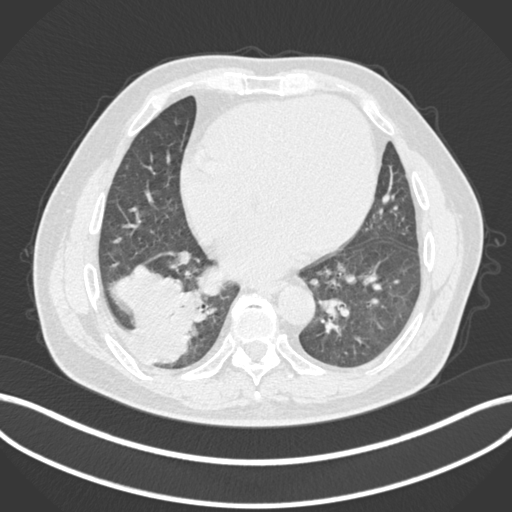
Chest CT, one axial slice. Position 56 of 200 along the scan axis. Reconstruction kernel B30f. Lung window (W 1500 / L -600 HU). 1 mm slice thickness. 512 × 512 image matrix. Patient: male, 59 years.
Annotated regions visible in this slice (rectangle marked by the reading radiologist):
- lung tumour (recorded histology: adenocarcinoma): bounding box [x1, y1, x2, y2] px = [105, 256, 210, 367]